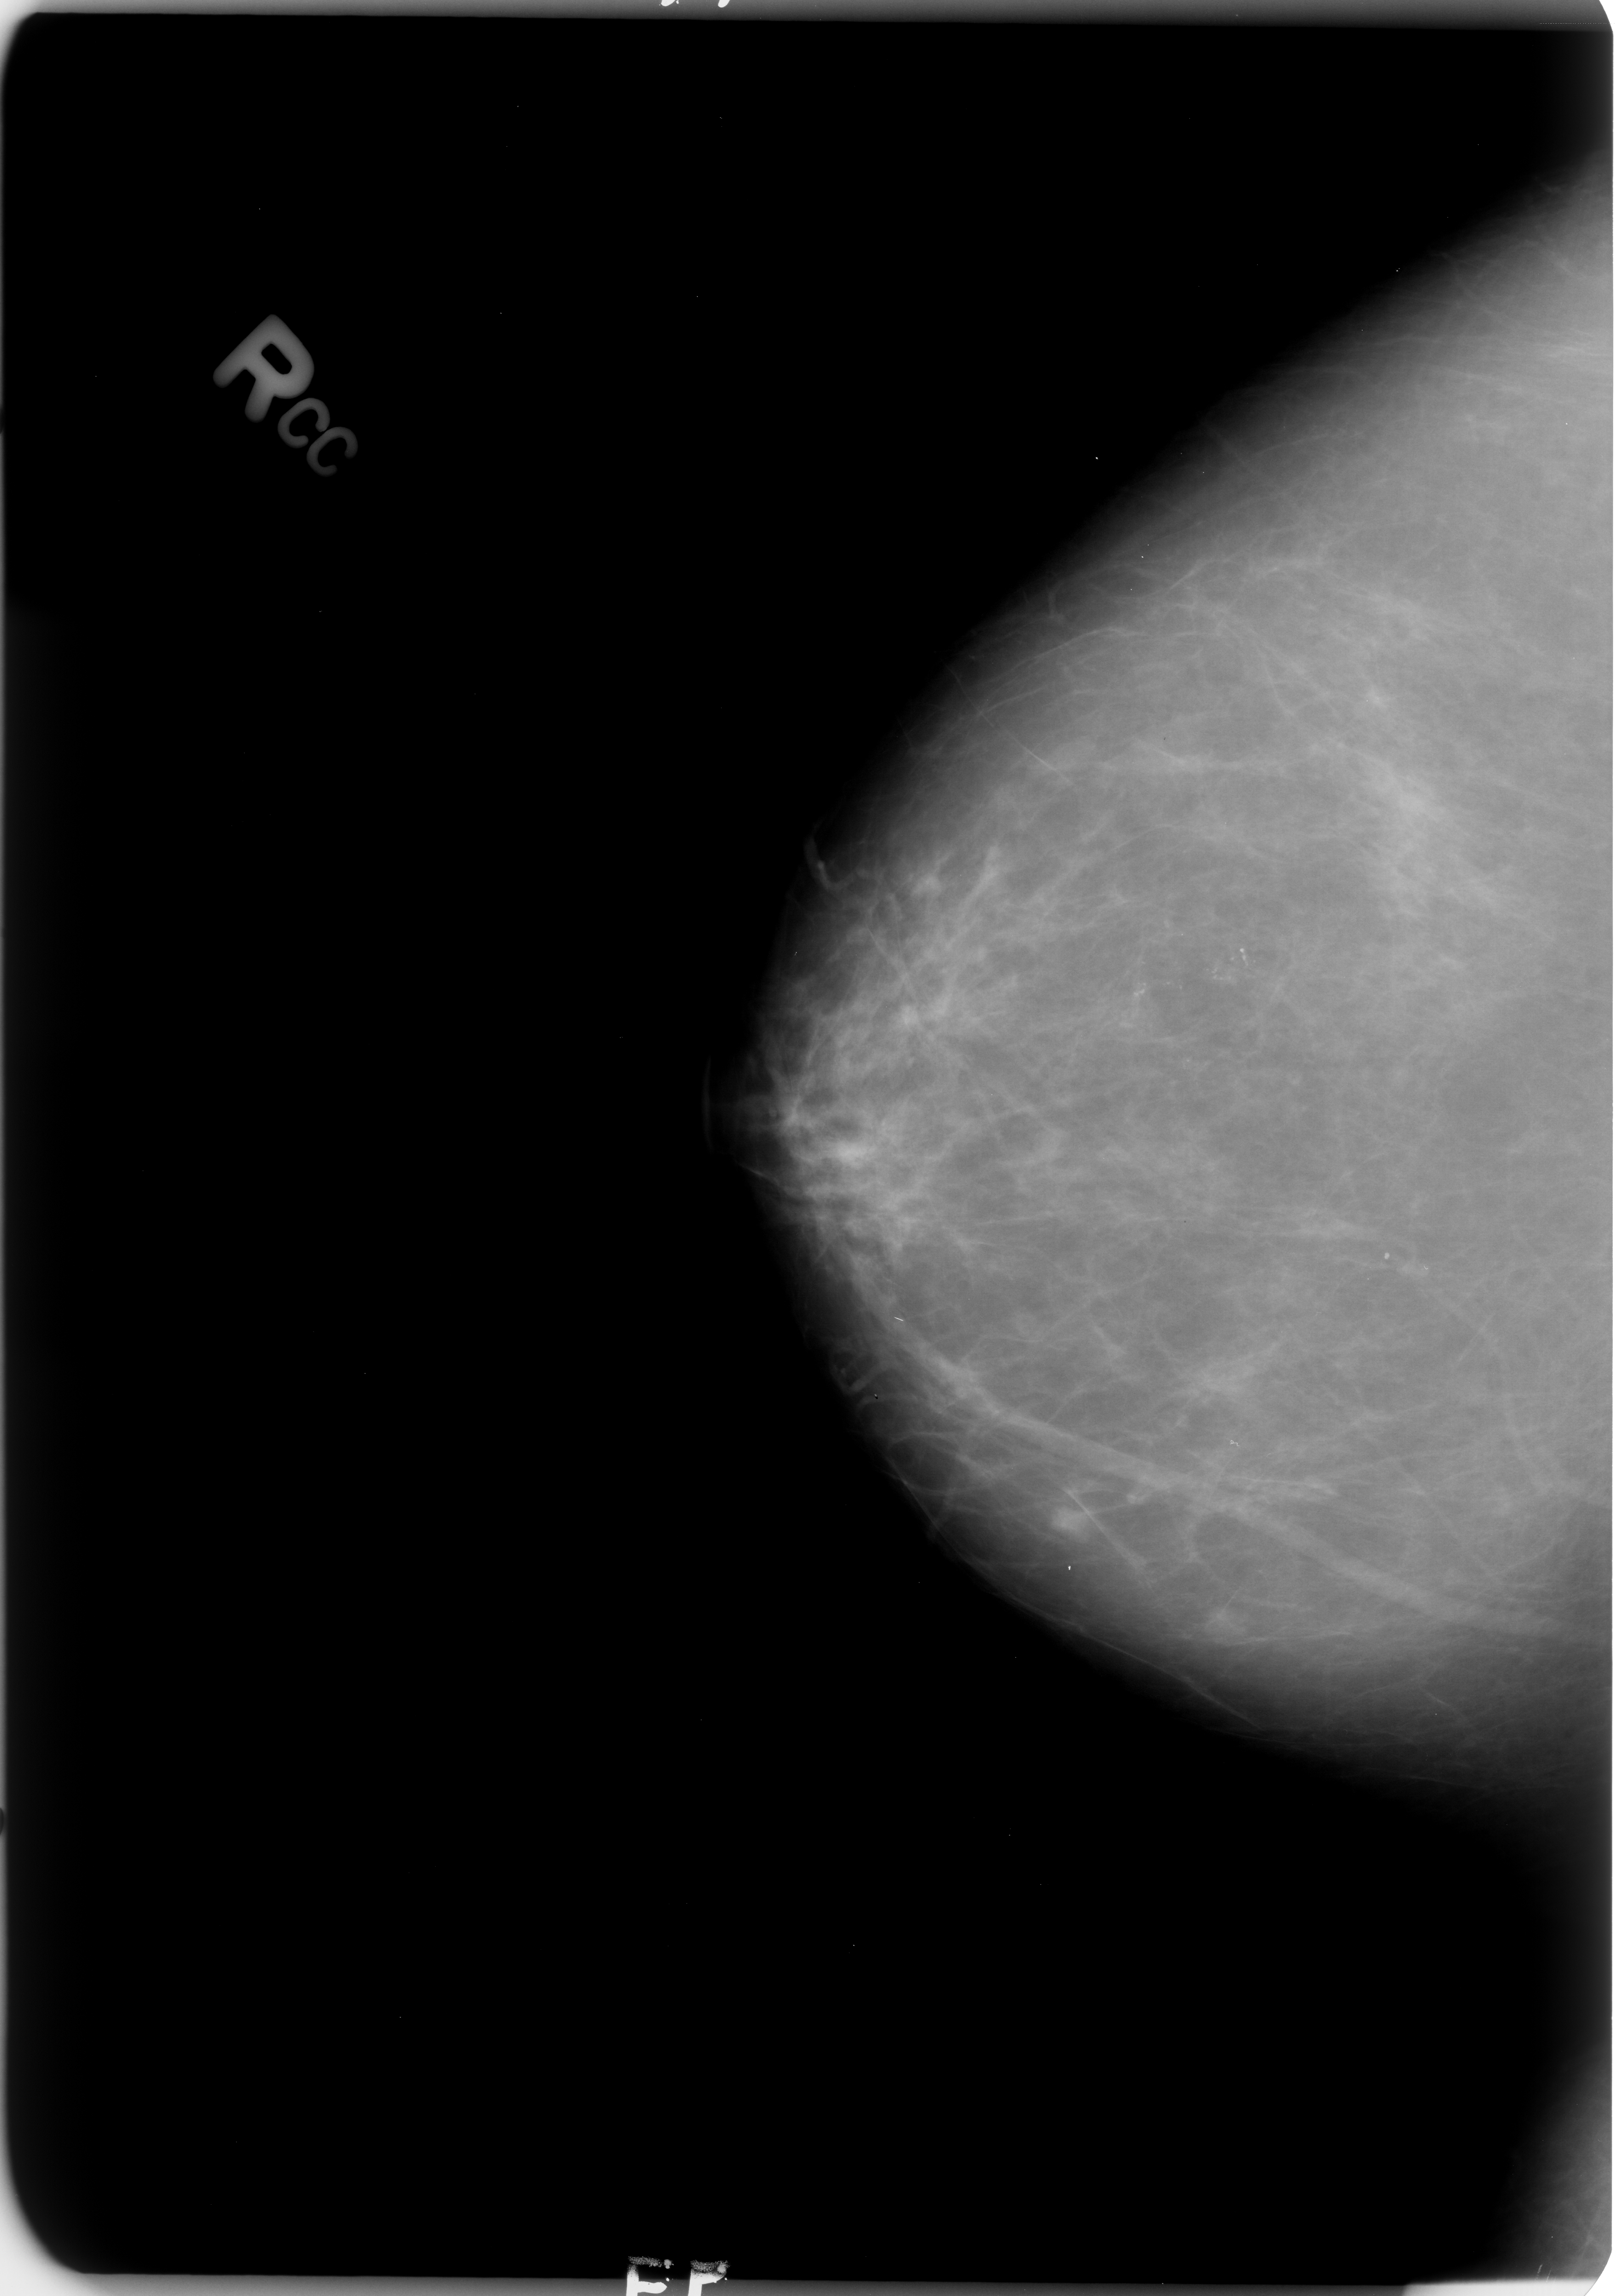
Mammogram (digitized film); right breast; craniocaudal (CC) view.
Marked findings (only marked abnormalities are described; nothing is implied about the rest of the image): Finding 1 of 2: calcifications, morphology pleomorphic, distribution clustered; BI-RADS assessment category 4; pathology (as recorded): malignant. Finding 2 of 2: calcifications, morphology pleomorphic, distribution clustered; BI-RADS assessment category 4; pathology result (as recorded, not read from the image): malignant.